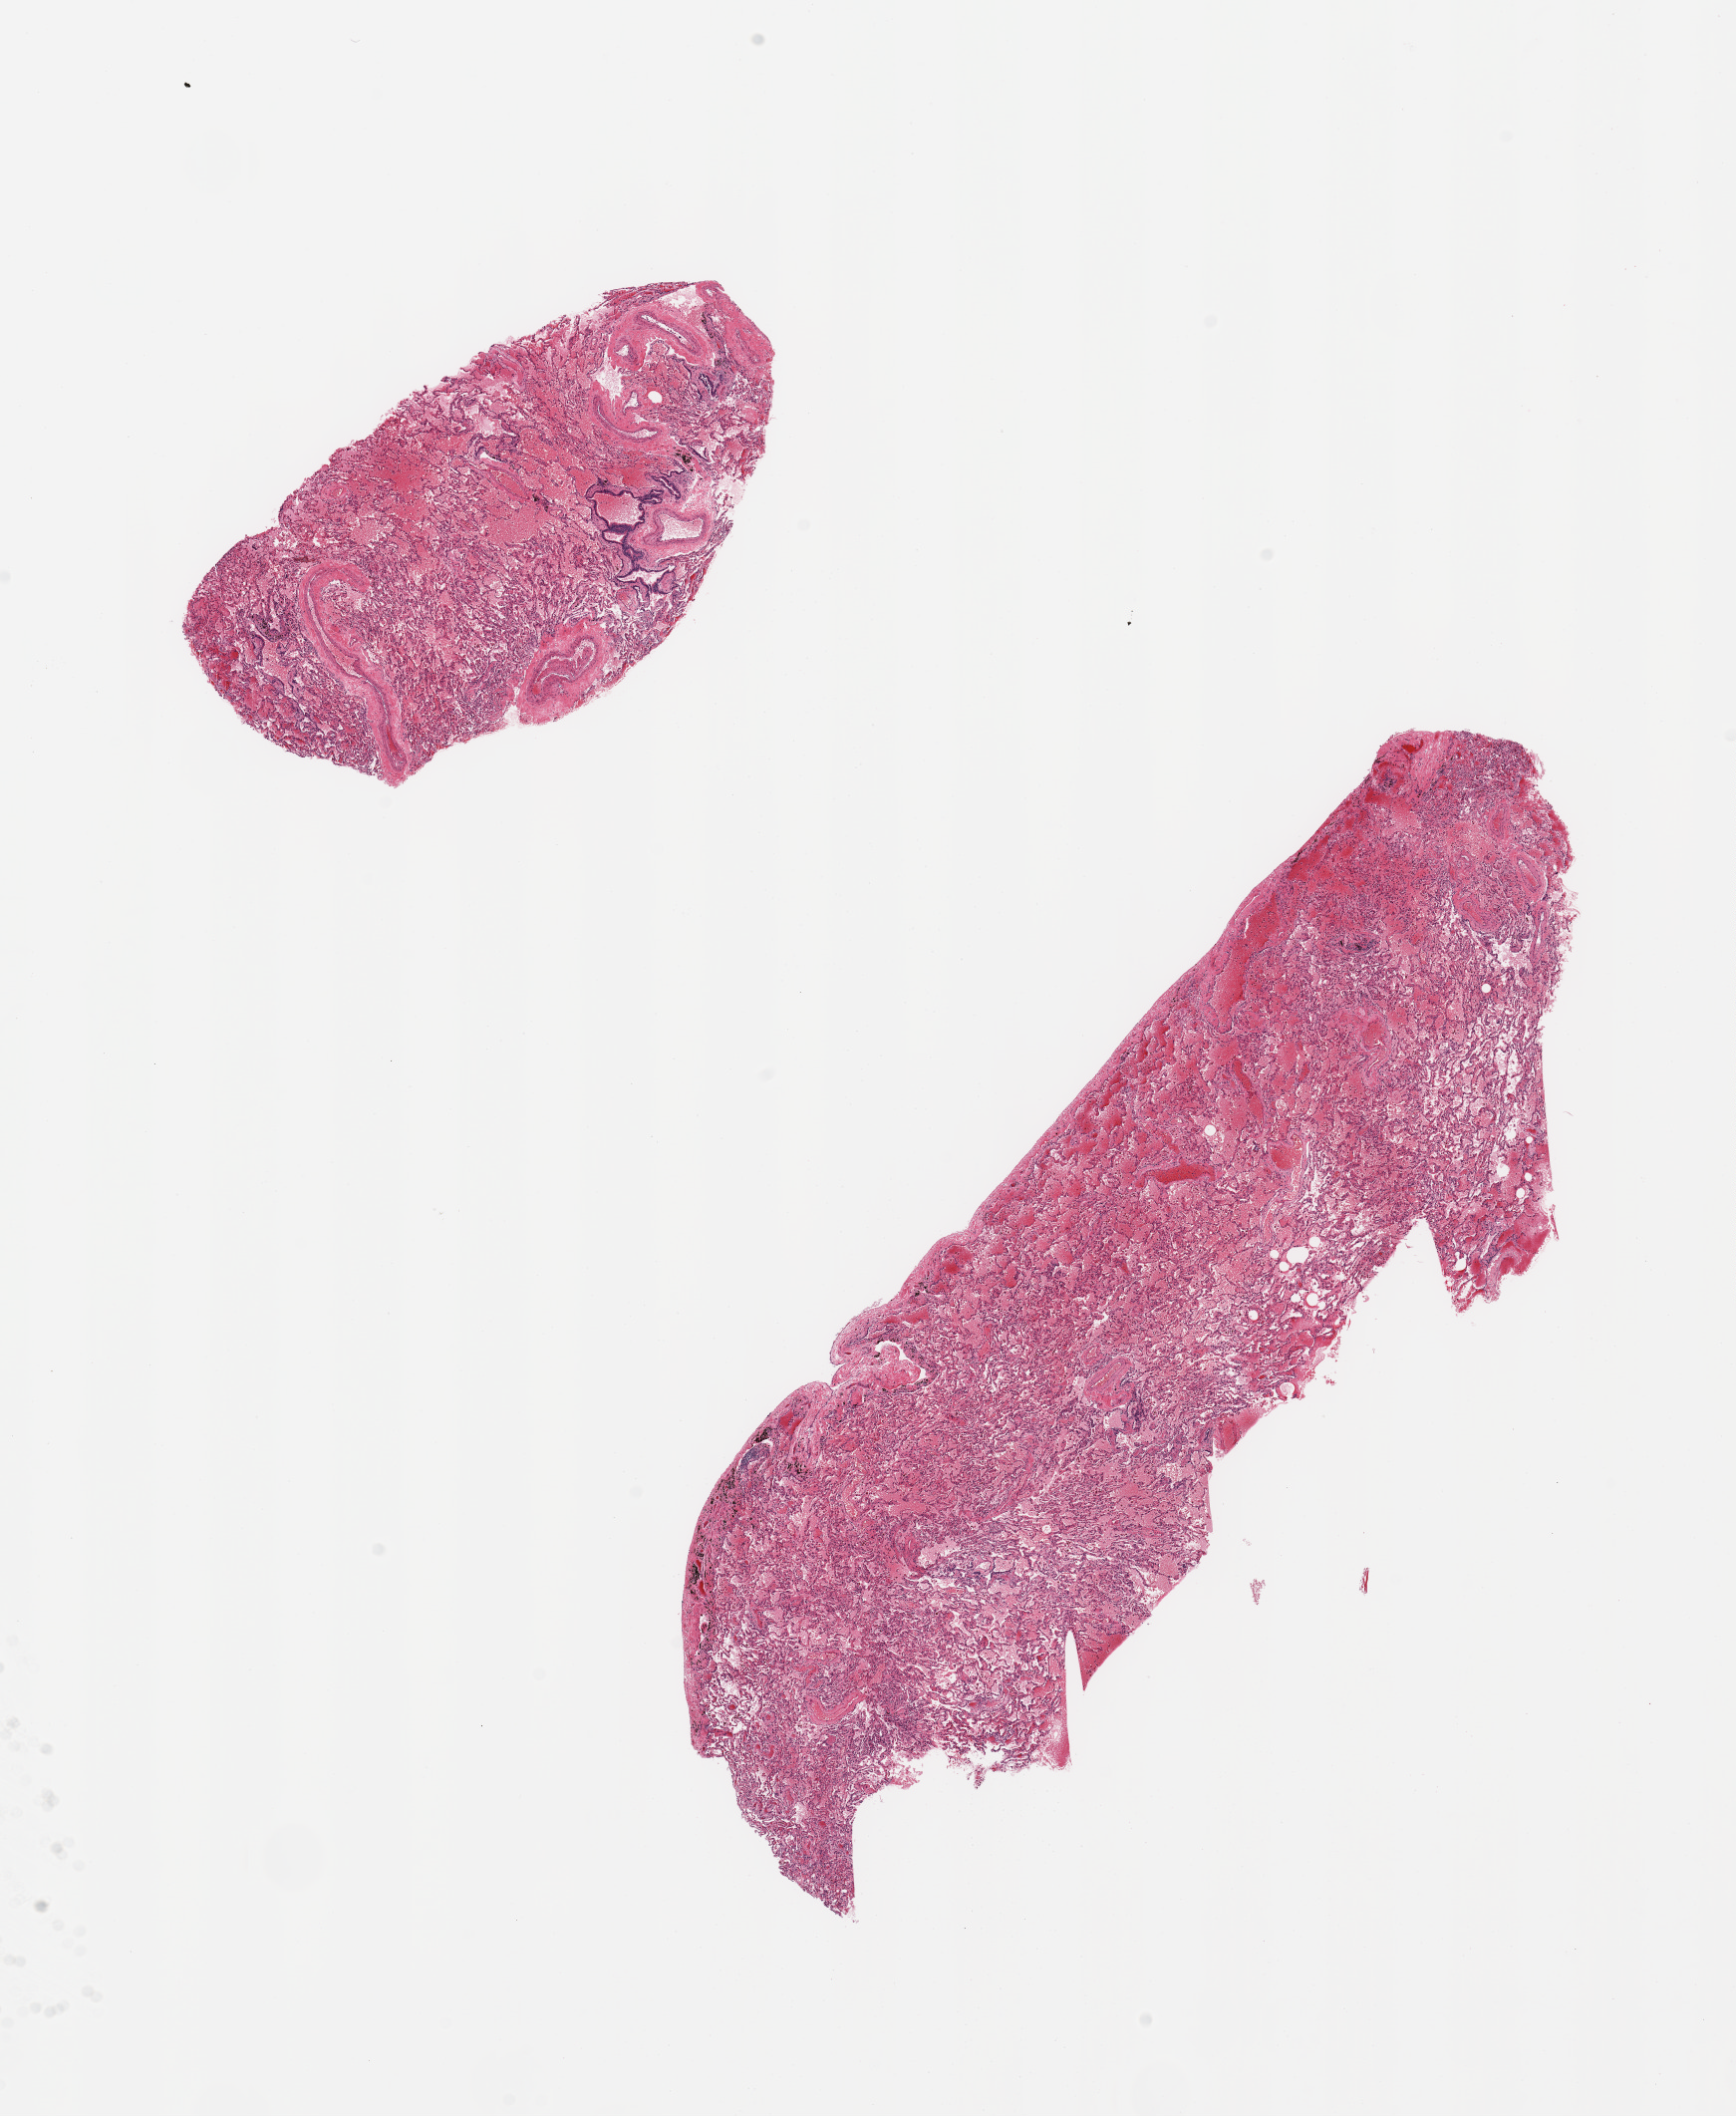
Whole-slide image, hematoxylin and eosin (H&E) stain, brightfield — a low-resolution overview of the entire scanned area, about 13.8 x 16.8 mm (acquisition: 20x scan); PAXgene-fixed, paraffin-embedded tissue; sampled site (target tissue): lung; donor tissue sample.
- reviewer comment on this tissue sample: 2 pieces; marked congestion: anthracosis